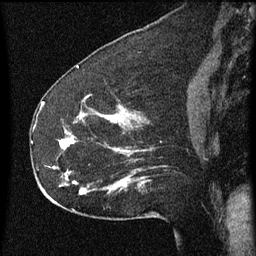
Breast MRI (dynamic contrast-enhanced), one sagittal slice; dynamic contrast-enhanced series, image 2 of 3 at this slice position (ordered by acquisition); 1.5 T; TE 4.2 ms, TR 8 ms; 2 mm slice thickness; 256 × 256 image matrix. Patient: female, 52 years.
Structures marked on this image (semi-automatic segmentation, software-assisted and operator-edited):
- analysis volume of interest (the breast-tissue region the enhancement analysis was run in; not a lesion): bounding box [x1, y1, x2, y2] px = [54, 110, 162, 207]
- tumour enhancement mask (voxels above the 70 % enhancement threshold inside the analysis volume of interest): [59, 116, 128, 193]